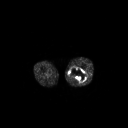
FDG PET of an extremity soft-tissue mass (from a PET/CT study), one axial slice; slice 216 of 267 in the series (ordered by position); 128 × 128 image matrix, field of view 700 × 700 mm. Male patient, age 44 years. From the clinical record (not read from this slice): histological type: undifferentiated pleomorphic liposarcoma; grade: high; site of the primary tumour: left thigh.
Outlined on this slice (expert contour drawn on MRI and transferred to this co-registered scan by the dataset authors):
- gross tumour volume including surrounding oedema: bounding box (x1, y1, x2, y2) in pixels: (69, 66, 87, 83)
- gross tumour volume (mass): (69, 68, 87, 83)